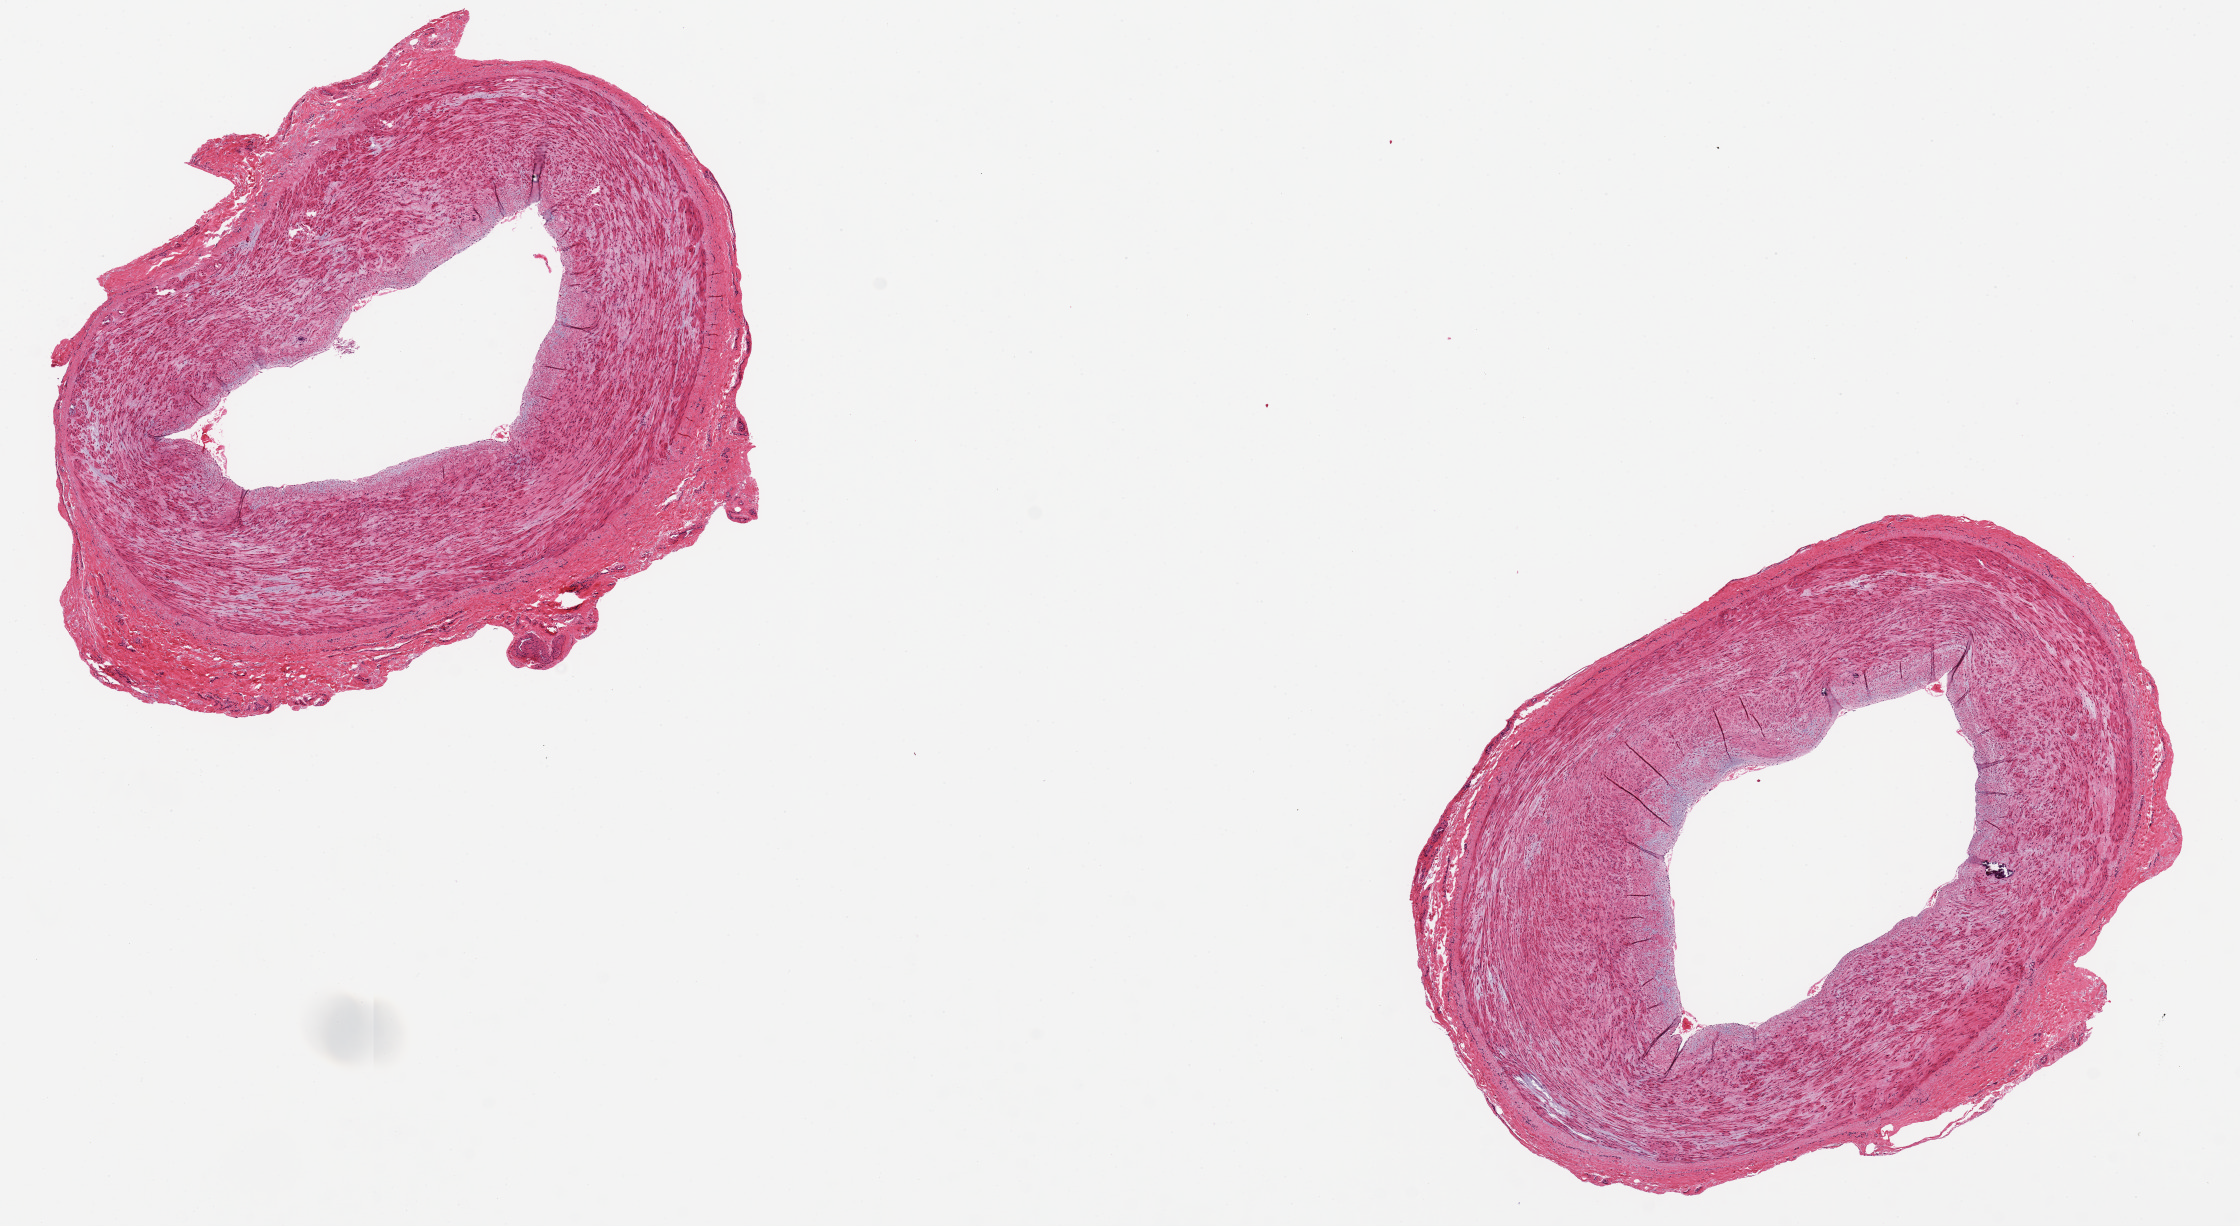
Digitized haematoxylin and eosin-stained section — whole scanned area (about 17.7 x 9.7 mm) shown as a low-resolution overview; PAXgene-fixed, paraffin-embedded tissue; section of tibial artery (target tissue); donor tissue sample. Male donor.
Reviewer comment on this tissue sample: Minimal intimal thickening, small focal calcification, no surrounding fat.